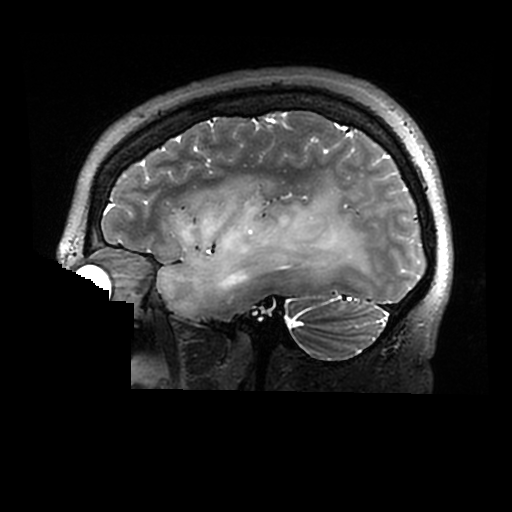
Brain MRI from a brain-tumour surgery series, one sagittal slice; slice 215 of 320 in the series (ordered by position); 0.6 mm slice thickness; 512 × 512 image matrix. From the clinical record (not read from this slice): histopathology: Astrocytoma; WHO grade: 2; IDH mutation: yes.
Annotated regions visible in this slice (outlined manually by an expert reader):
- tumour: bounding box [x1, y1, x2, y2] px = [157, 185, 375, 313]